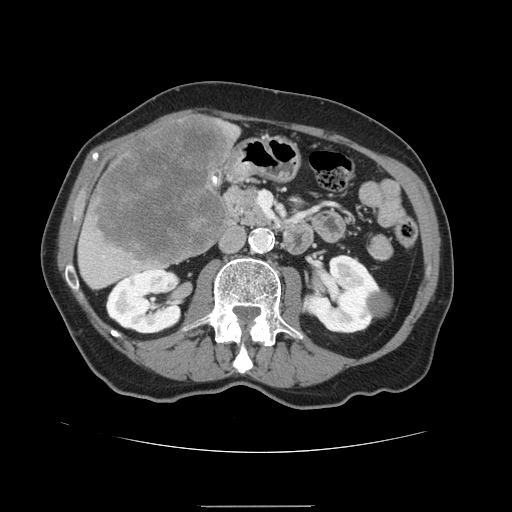
Contrast-enhanced abdominal CT, one axial slice; position 56 of 168 along the scan axis; 120 kVp; intravenous contrast given; soft-tissue window (W 400 / L 40 HU); 2.5 mm slice thickness; 512 × 512 image matrix, field of view 386 × 386 mm. Male patient, age 74 years. Case-level facts recorded for this patient, not image findings: diagnosis: colorectal cancer liver metastases, imaged before liver resection; multiple liver metastases: no; largest metastasis: 14.5 cm; disease in both lobes: yes.
Structures marked on this image (outlined manually by an expert reader):
- liver: bounding box [x1, y1, x2, y2] px = [77, 114, 241, 290]
- liver metastasis: [90, 118, 231, 266]